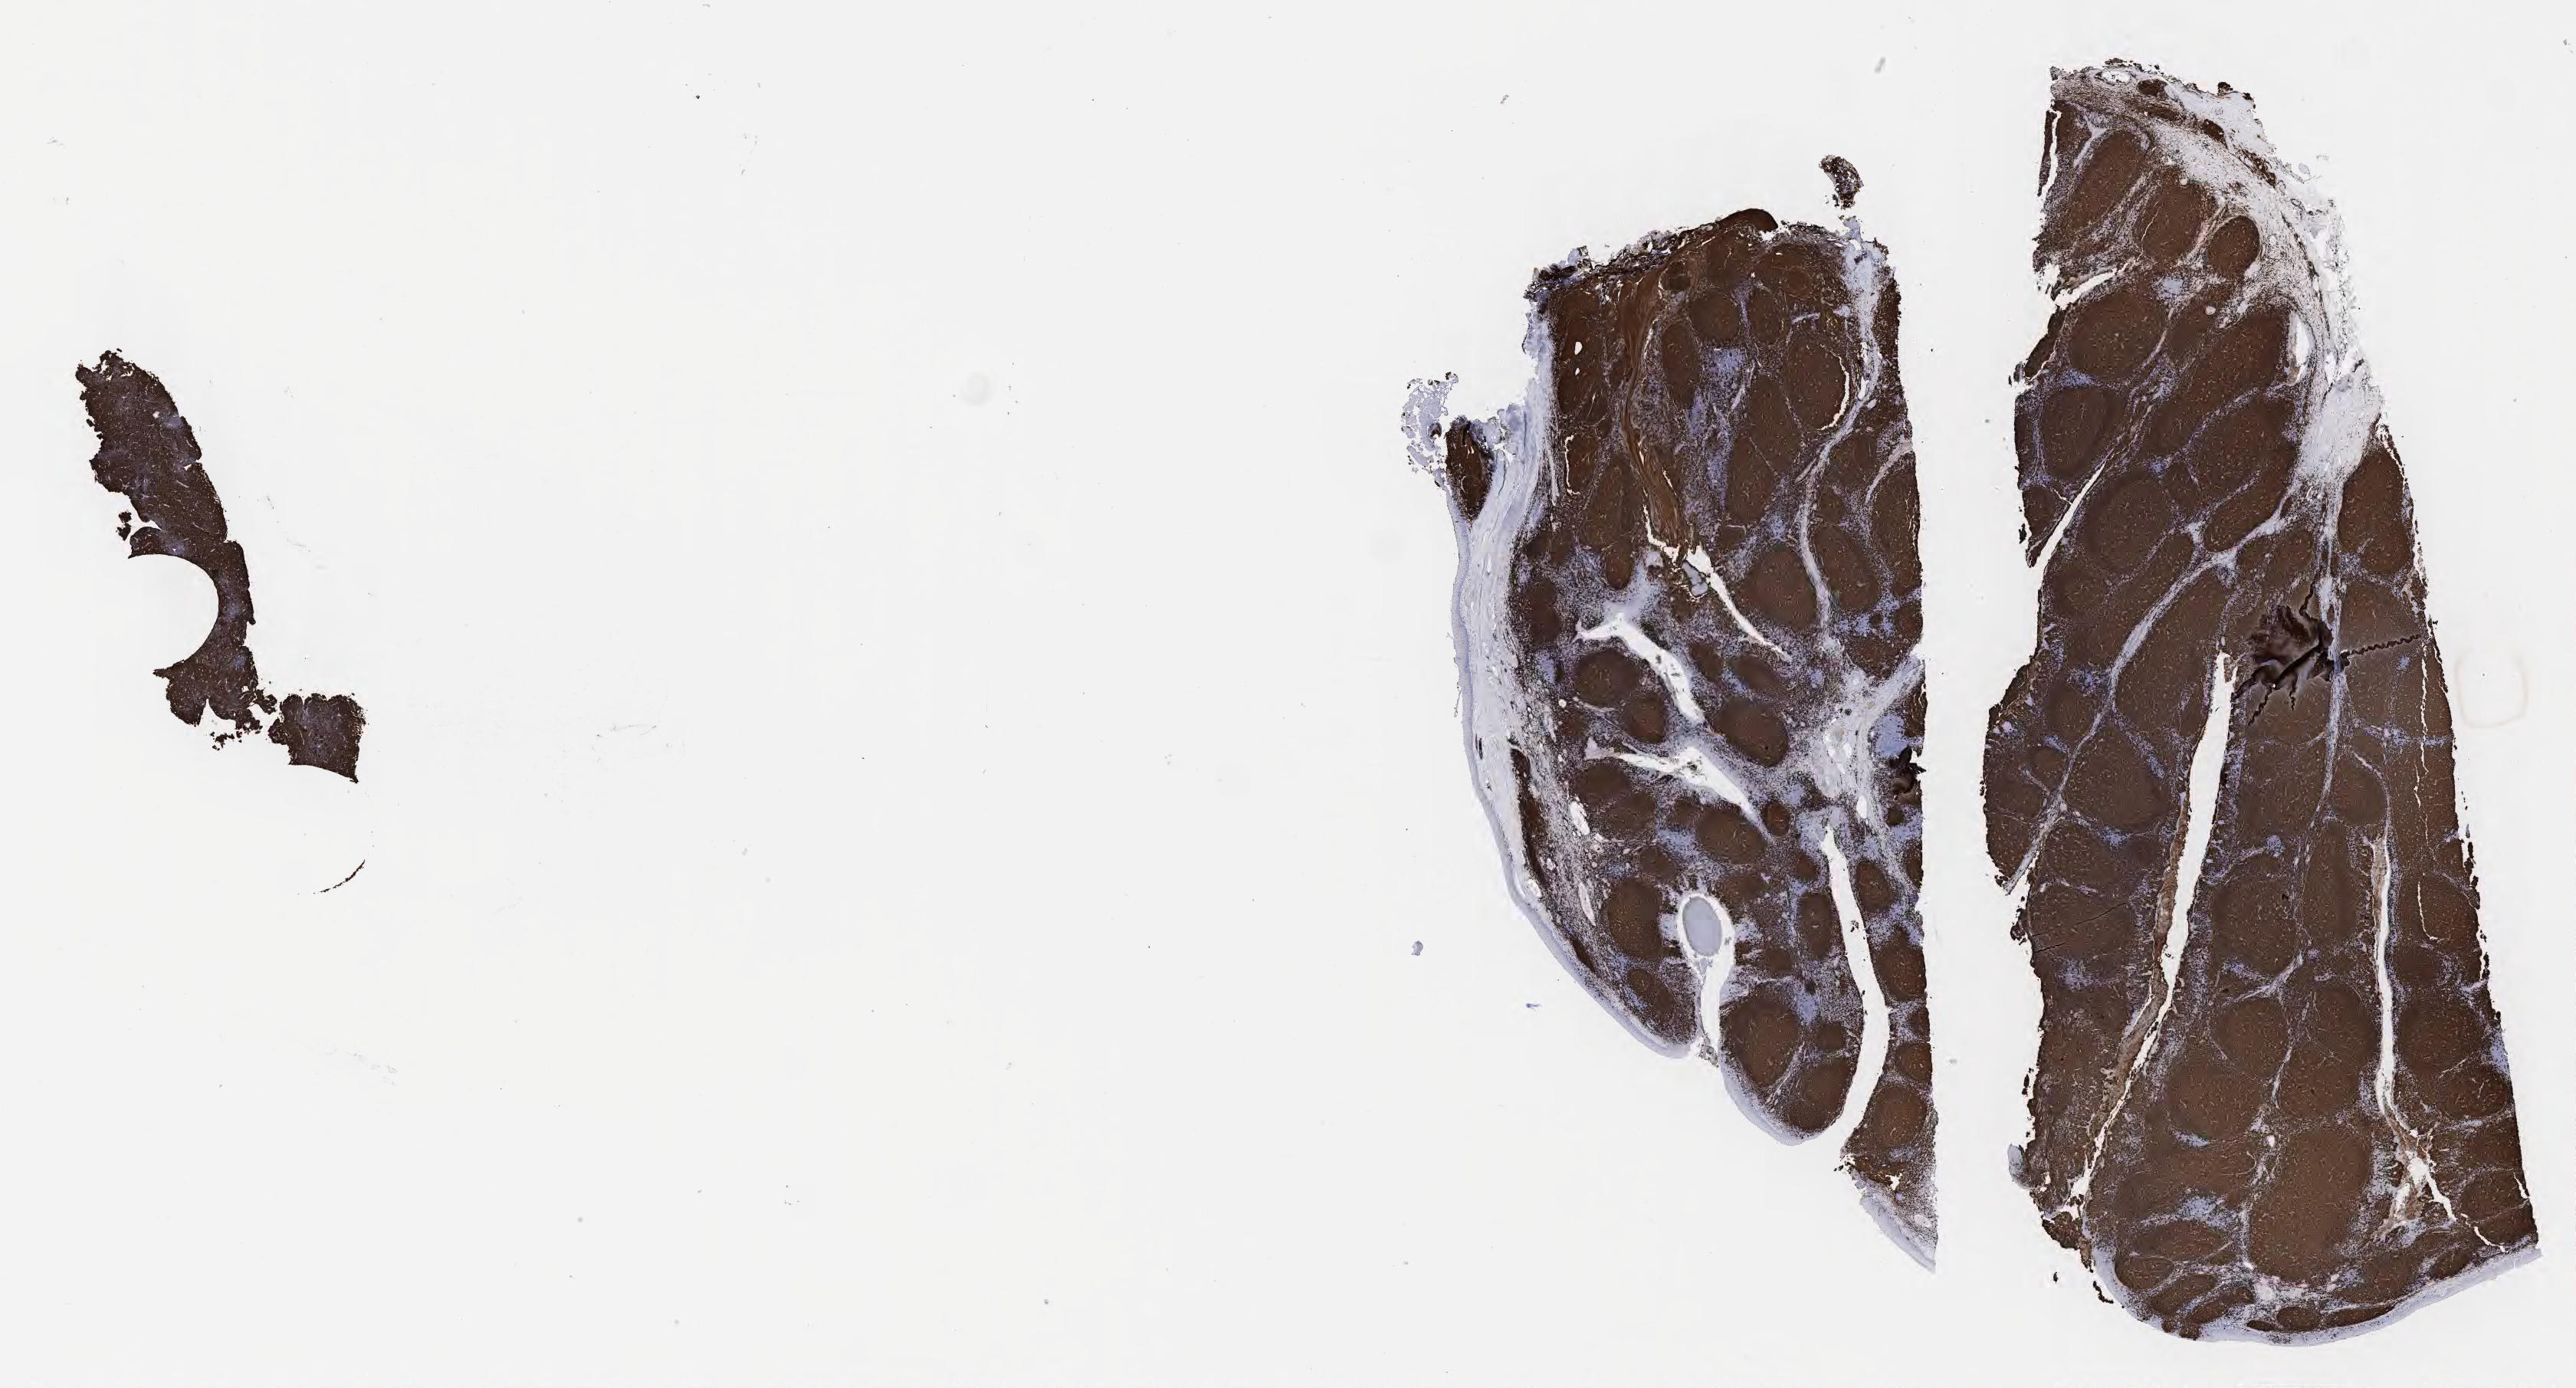
Whole-slide image, immunohistochemical stain for CD20, a low-resolution overview of the entire scanned area, about 27.2 x 14.6 mm. Specimen: tumor tissue. Male patient; age at initial diagnosis 5 years.
Diagnosis: Burkitt lymphoma, NOS.